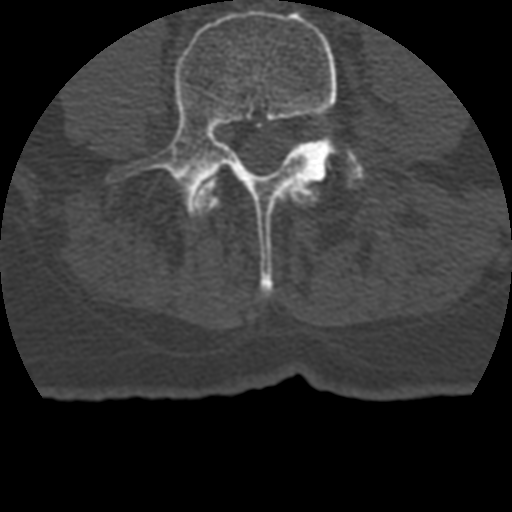
CT including the spine, one axial slice; position 67 of 399 along the scan axis; reconstruction kernel STANDARD; bone window (W 1800 / L 400 HU); 512 × 512 image matrix. Patient age 69 years. From the clinical record (not read from this slice): primary cancer: prostate.
Structures marked on this image (semi-automatically segmented with operator editing):
- L3 vertebra: bounding box [x1, y1, x2, y2] px = [194, 180, 317, 214]
- L4 vertebra: [108, 10, 359, 297]
- L5 vertebra: [346, 161, 364, 187]